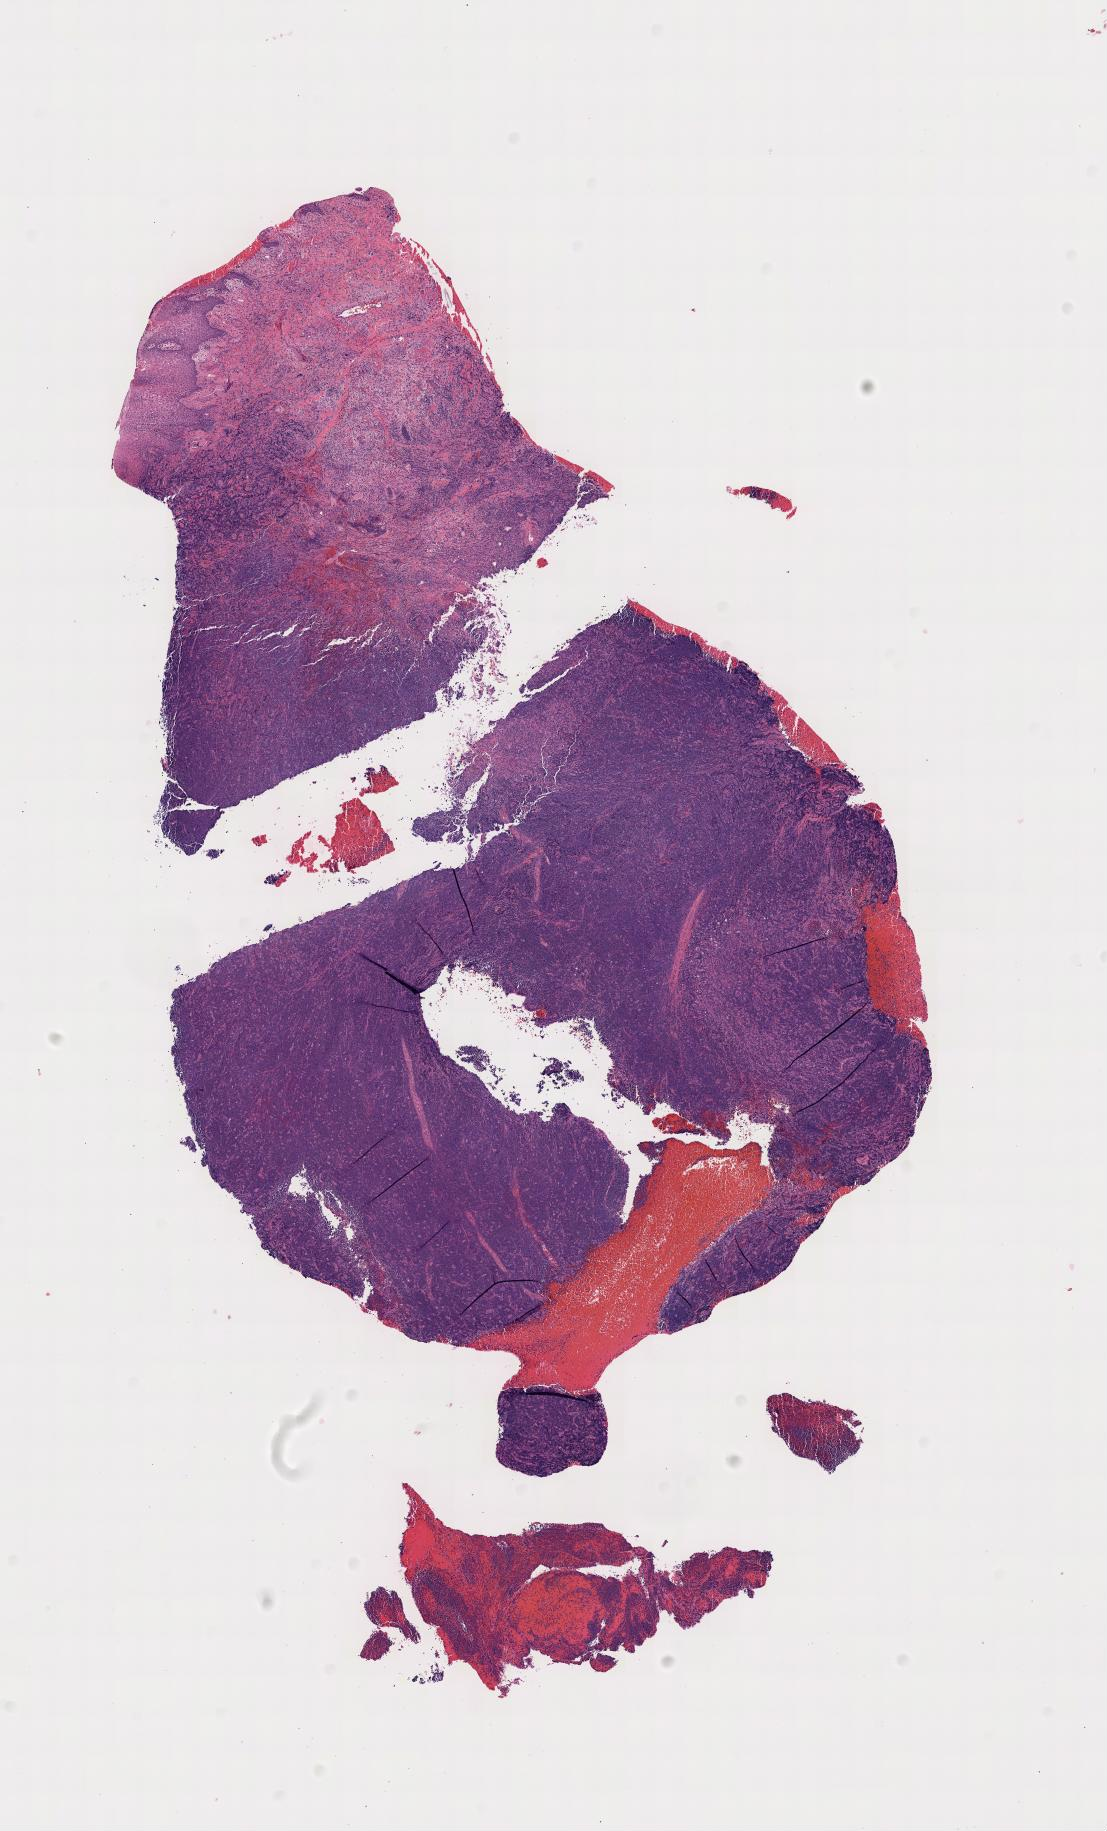
Whole-slide image, haematoxylin and eosin stain — whole scanned area shown as a low-resolution overview; tumor tissue; anatomic site: cranium. Male patient, age 12 years.
Histologic diagnosis: Burkitt lymphoma, NOS.